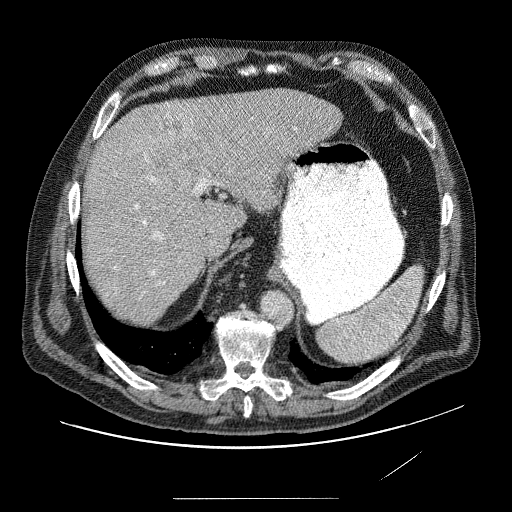
Contrast-enhanced abdominal CT (liver protocol), one axial slice. Position 59 of 89 along the scan axis. Reconstruction kernel STANDARD. 120 kVp. Soft-tissue window (W 400 / L 40 HU). 2.5 mm slice thickness. 512 × 512 image matrix, field of view 420 × 420 mm. From the clinical record (not read from this slice): diagnosis: hepatocellular carcinoma (patient treated with transarterial chemoembolisation; whether this scan precedes or follows treatment is not stated here); TNM stage (as recorded): Stage-IVA; Child-Pugh class: A; tumour nodularity: multinodular.
Outlined on this slice (semi-automatic segmentation, software-assisted and operator-edited):
- liver parenchyma outside the tumour (the mass and vessels are separate outlines, so this box may not span the whole liver): bounding box [x1, y1, x2, y2] px = [84, 88, 344, 306]
- mass: [98, 106, 280, 288]
- liver vessels: [126, 119, 329, 288]